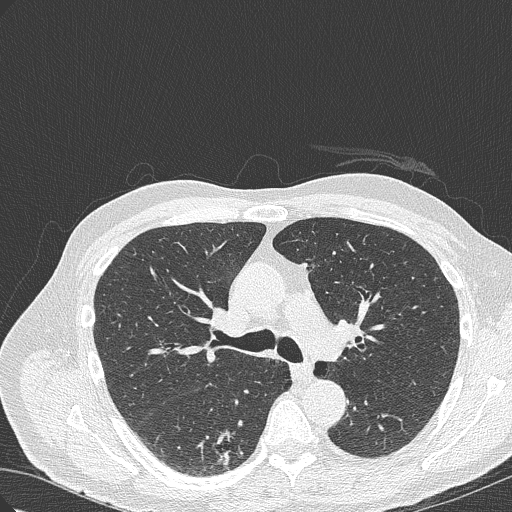
Axial slice from a low-dose chest CT screening exam. First (baseline) screen. Lung window (W 1500 / L -600 HU). 1 mm slice thickness. Slice 115 of 322 in the series. 512 × 512 image matrix. Male participant, aged 70 years at enrolment. Current smoker at enrolment.
- Expert reader's lesion annotation, box from (x=201, y=419) to (x=265, y=468) px.
- The screening reader recorded 4 non-calcified nodules or masses ≥4 mm on this exam (right lower lobe, right lower lobe, right upper lobe, right lower lobe); which of them this box marks is not recorded.
- Official screen result: positive, change unspecified: nodule(s) >= 4 mm or enlarging nodule(s), mass(es), or other non-specific abnormalities suspicious for lung cancer.
- Participant outcome: lung cancer diagnosed 978 days after this screen (after the third annual screen) — bronchiolo-alveolar adenocarcinoma, NOS, right lower lobe, poorly differentiated (G3), stage IB (AJCC 6th edition), 30 mm at pathology.